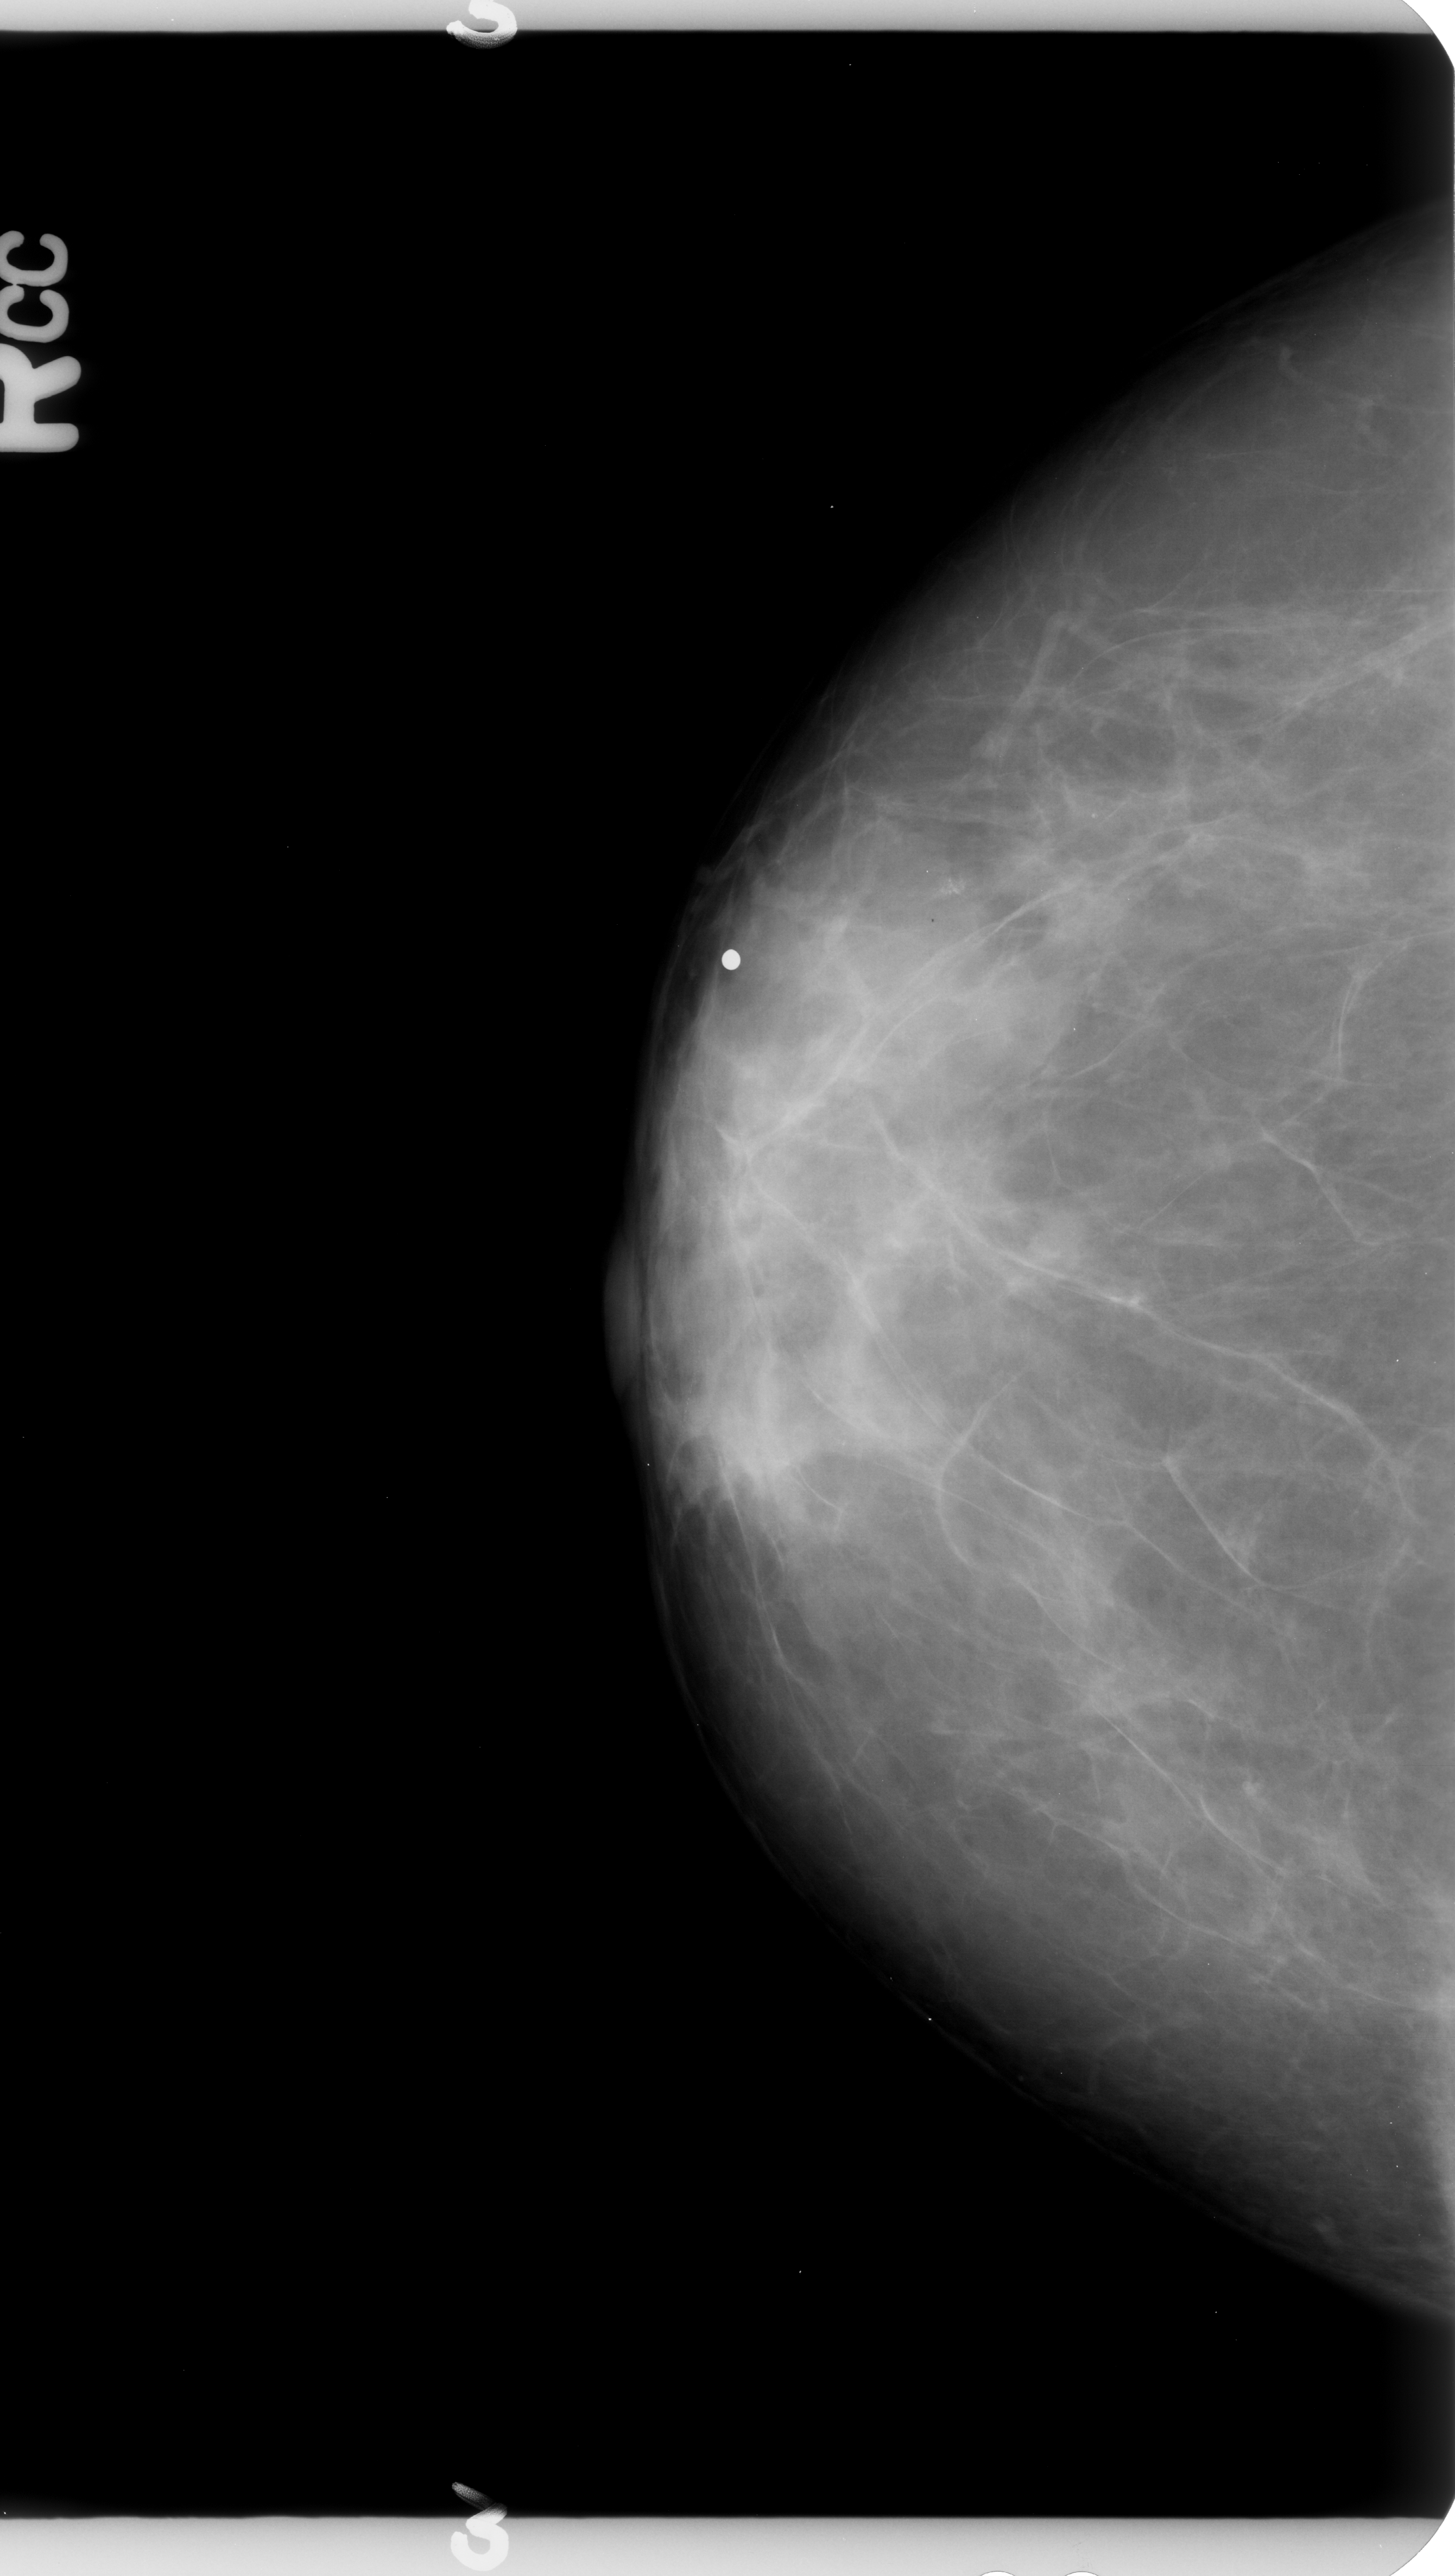
Mammogram (digitized film); right breast; CC view; BI-RADS breast density category 3 (scale 1–4); 1455 × 2576 image matrix.
Expert-marked regions of interest on this image (one box per marked abnormality):
- calcifications, morphology pleomorphic, distribution clustered; BI-RADS assessment category 4; pathology (as recorded): benign: bounding box [x1, y1, x2, y2] px = [881, 821, 1022, 957]